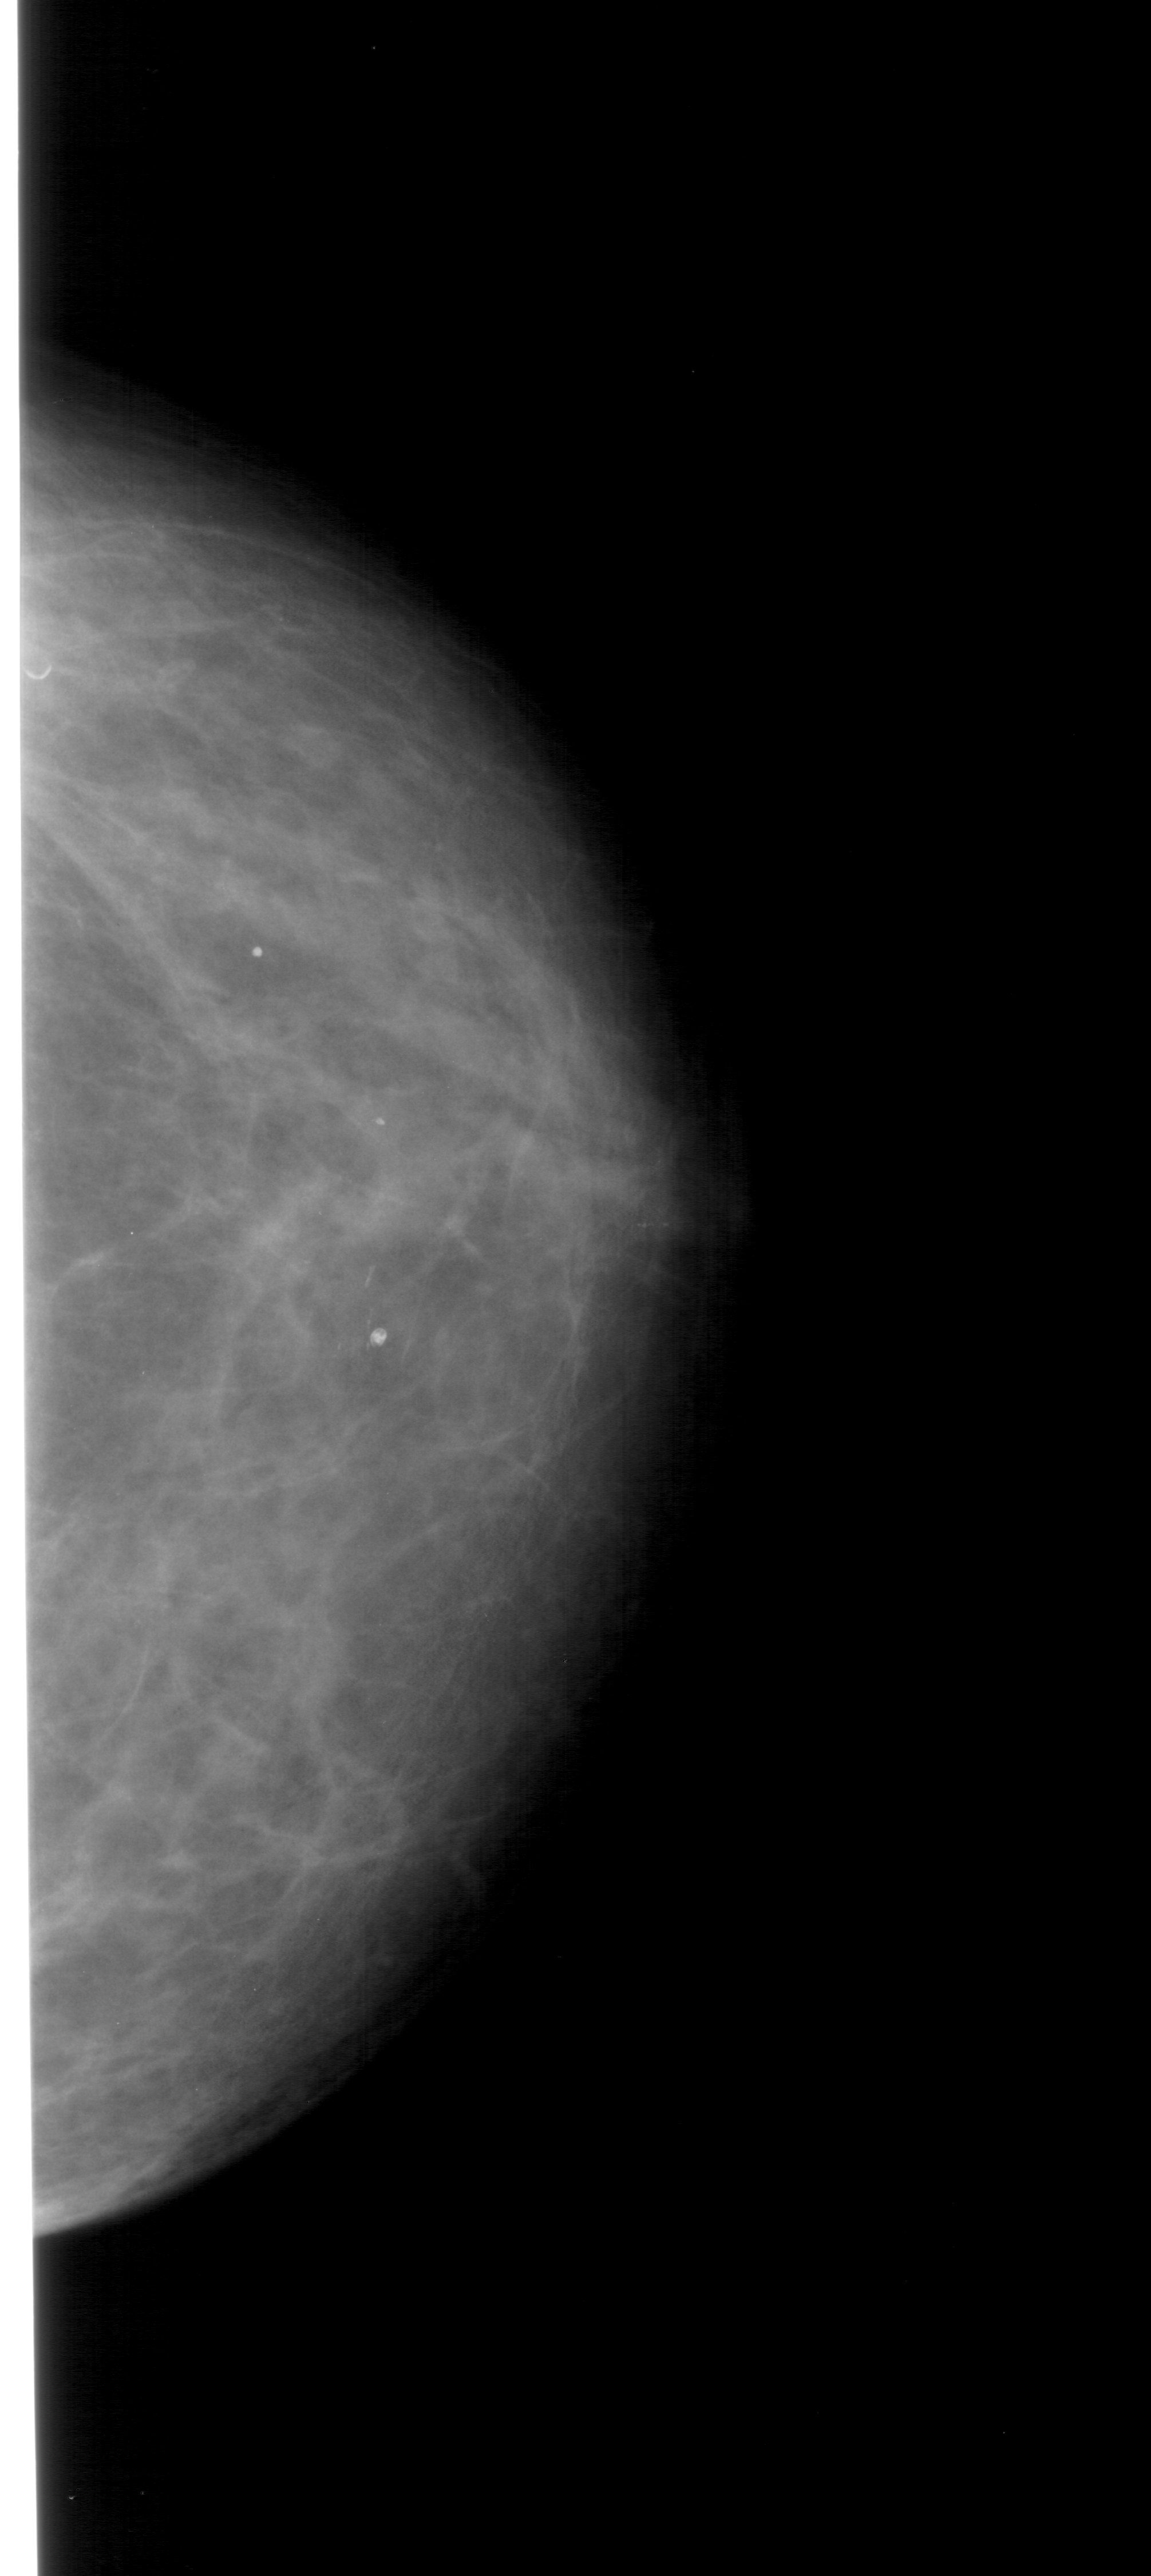
Scanned film-screen mammogram; right breast; CC view; BI-RADS breast density category 2 (scale 1–4); 1151 × 2576 image matrix.
Expert-marked regions of interest on this image (one box per marked abnormality):
- calcifications, morphology pleomorphic, distribution clustered; BI-RADS assessment category 4; subtlety rating 2 on a 1 (subtle) to 5 (obvious) scale; pathology result (as recorded, not read from the image): malignant: bounding box <322,1263,374,1393> (left, top, right, bottom; pixels)